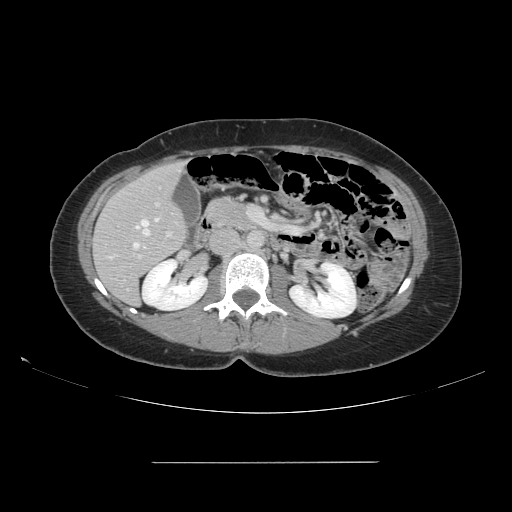
Contrast-enhanced abdominal CT, one axial slice. Position 70 of 151 along the scan axis. Intravenous contrast given. Soft-tissue window (W 400 / L 40 HU). 2.5 mm slice thickness. 512 × 512 image matrix, field of view 421 × 421 mm. Female patient, age 46 years. Case-level facts recorded for this patient, not image findings: diagnosis: colorectal cancer liver metastases, imaged before liver resection; multiple liver metastases: yes; largest metastasis: 3 cm; disease in both lobes: yes.
Structures marked on this image (outlined manually by an expert reader):
- hepatic veins: box from (x=133, y=218) to (x=159, y=249) px
- liver: (x=94, y=163)–(x=186, y=305)
- planned liver remnant (the part of the liver to remain after resection): (x=94, y=163)–(x=186, y=304)
- portal vein (with intrahepatic branches): (x=137, y=202)–(x=172, y=259)